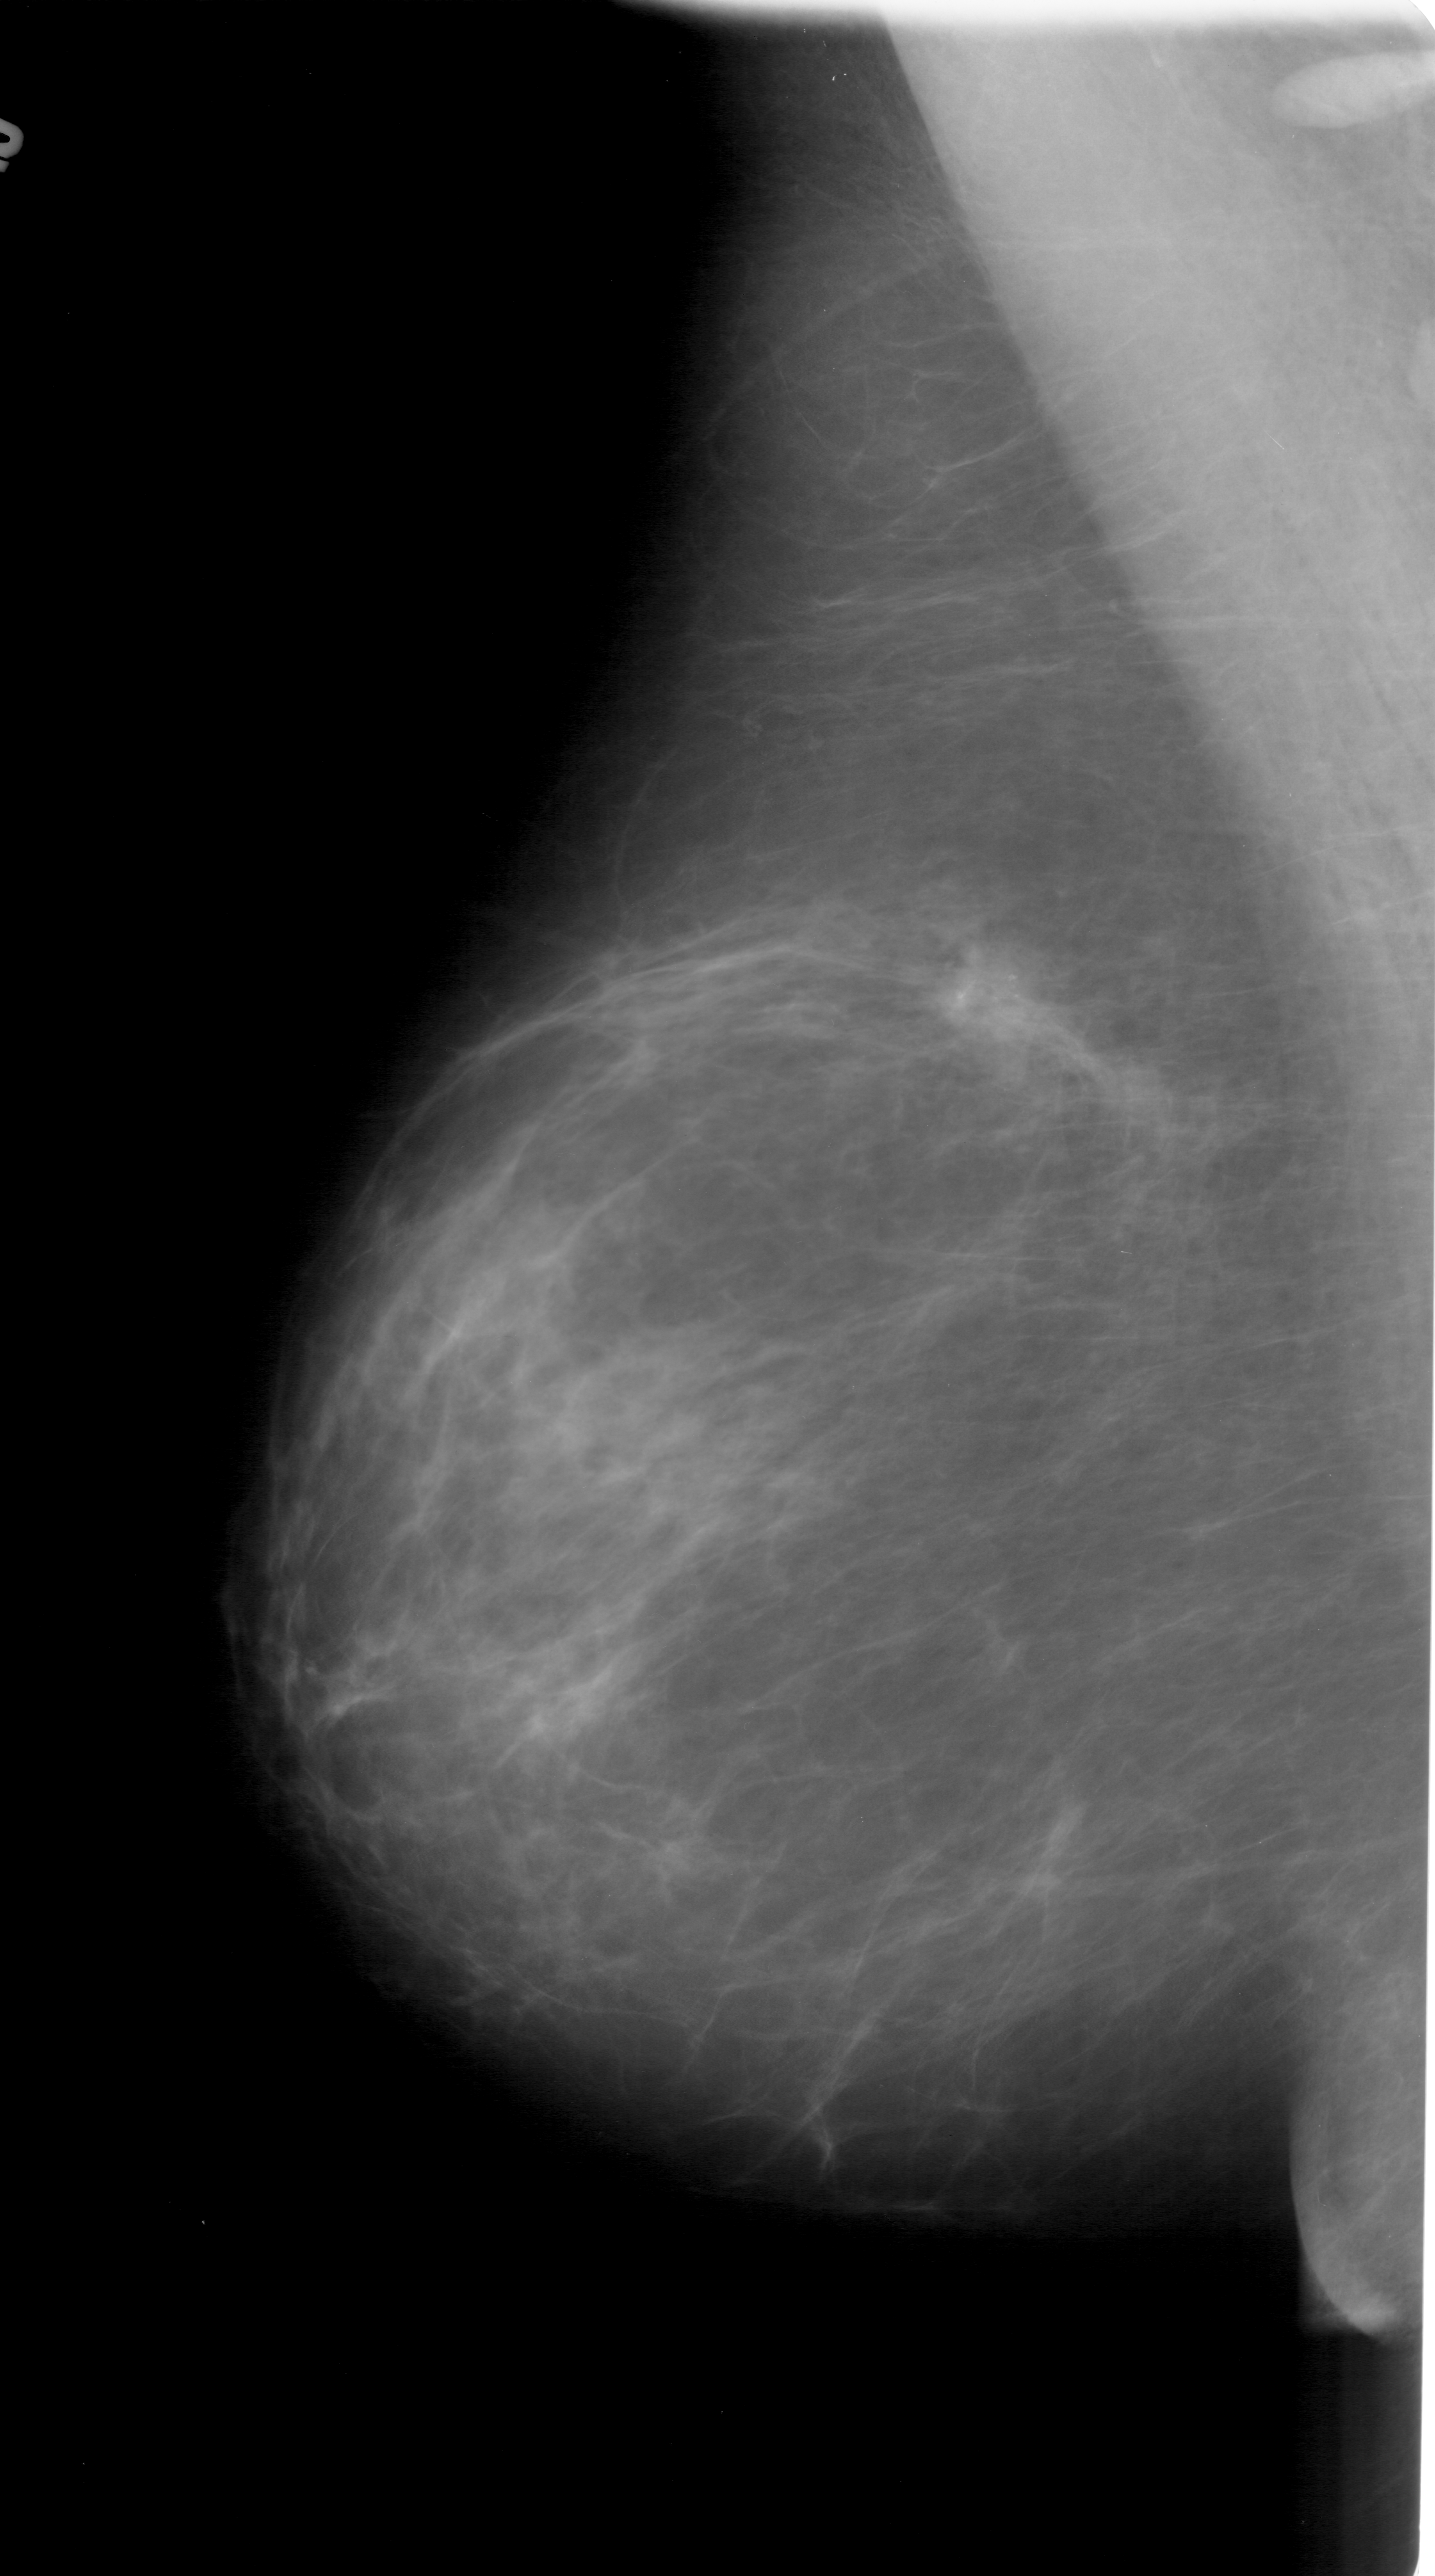
Digitized screen-film mammogram. Left breast. Mediolateral oblique (MLO) view. Breast composition: scattered fibroglandular densities (BI-RADS density category 2 of 4). 1435 × 2576 image matrix.
Marked abnormalities (boxes around the expert regions of interest):
- calcifications, morphology fine linear branching, distribution linear; BI-RADS assessment category 4; pathology result (as recorded, not read from the image): malignant: box from (x=945, y=964) to (x=1040, y=1031) px